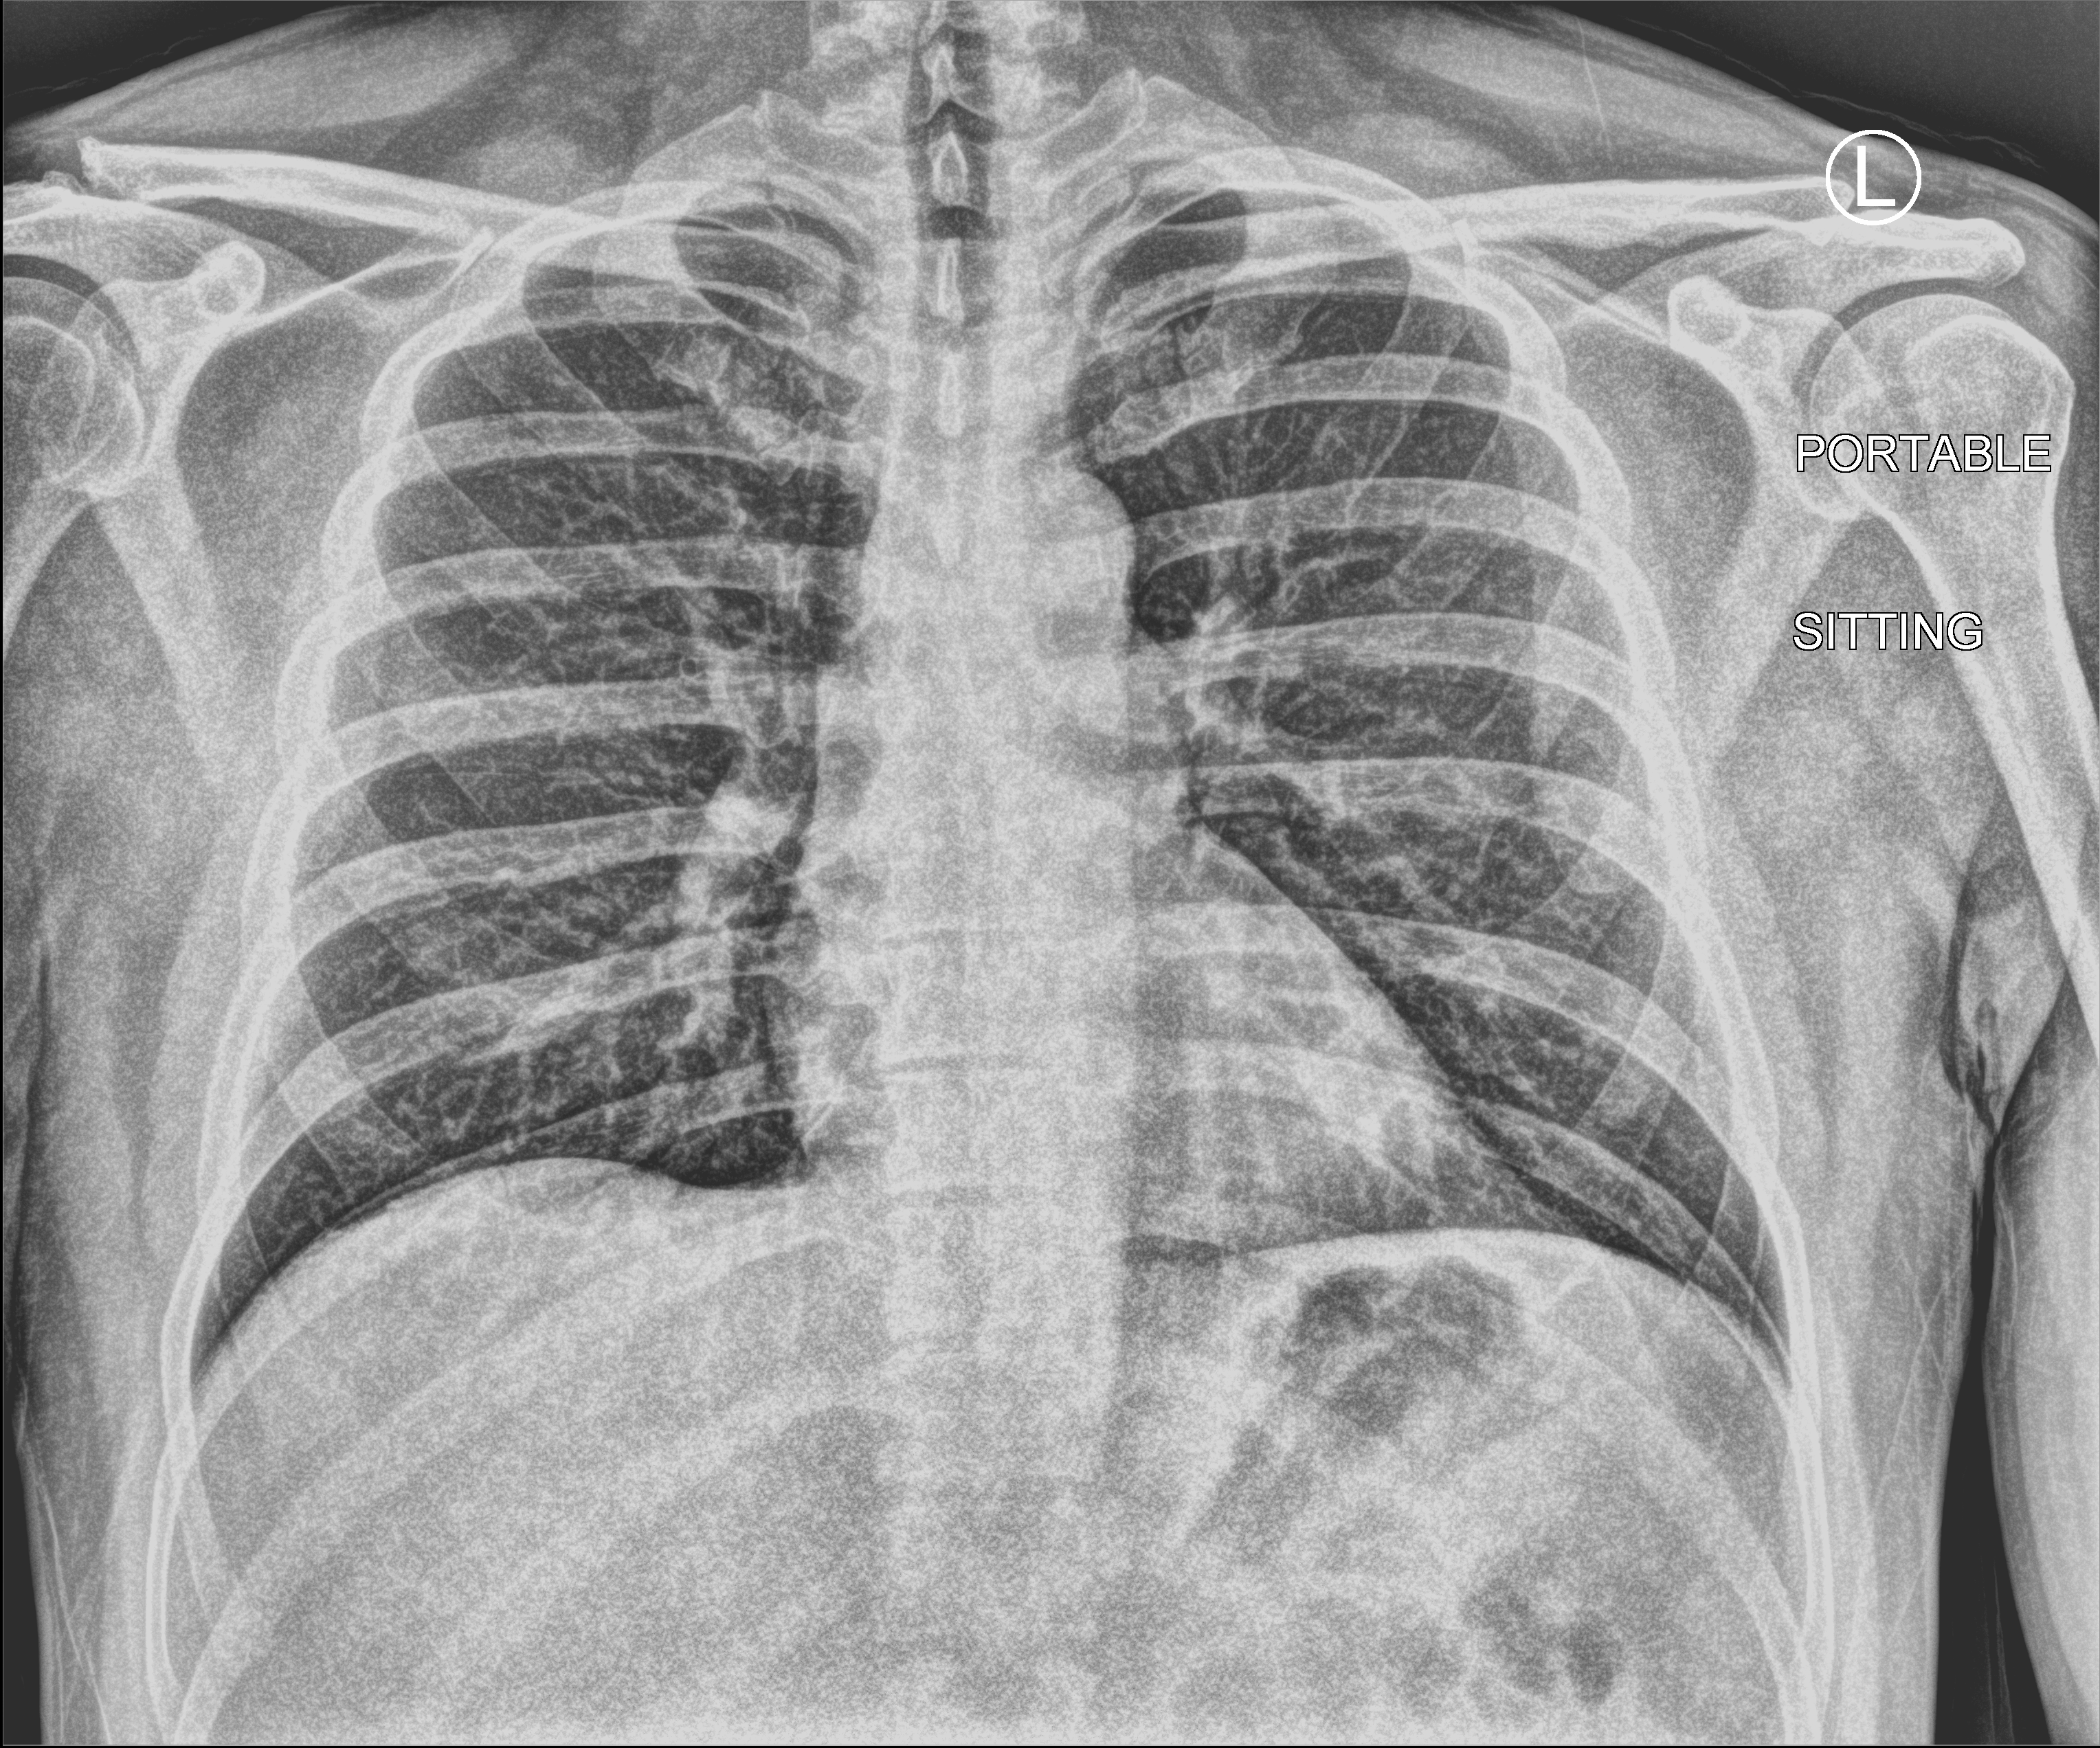
Bedside chest radiograph (computed radiography), anteroposterior (AP) projection. Male patient hospitalised with COVID-19, age 18–59 years.
Admission-level facts for this patient (not findings on this image; timing relative to this image not recorded): admitted to intensive care during this hospital stay: no.